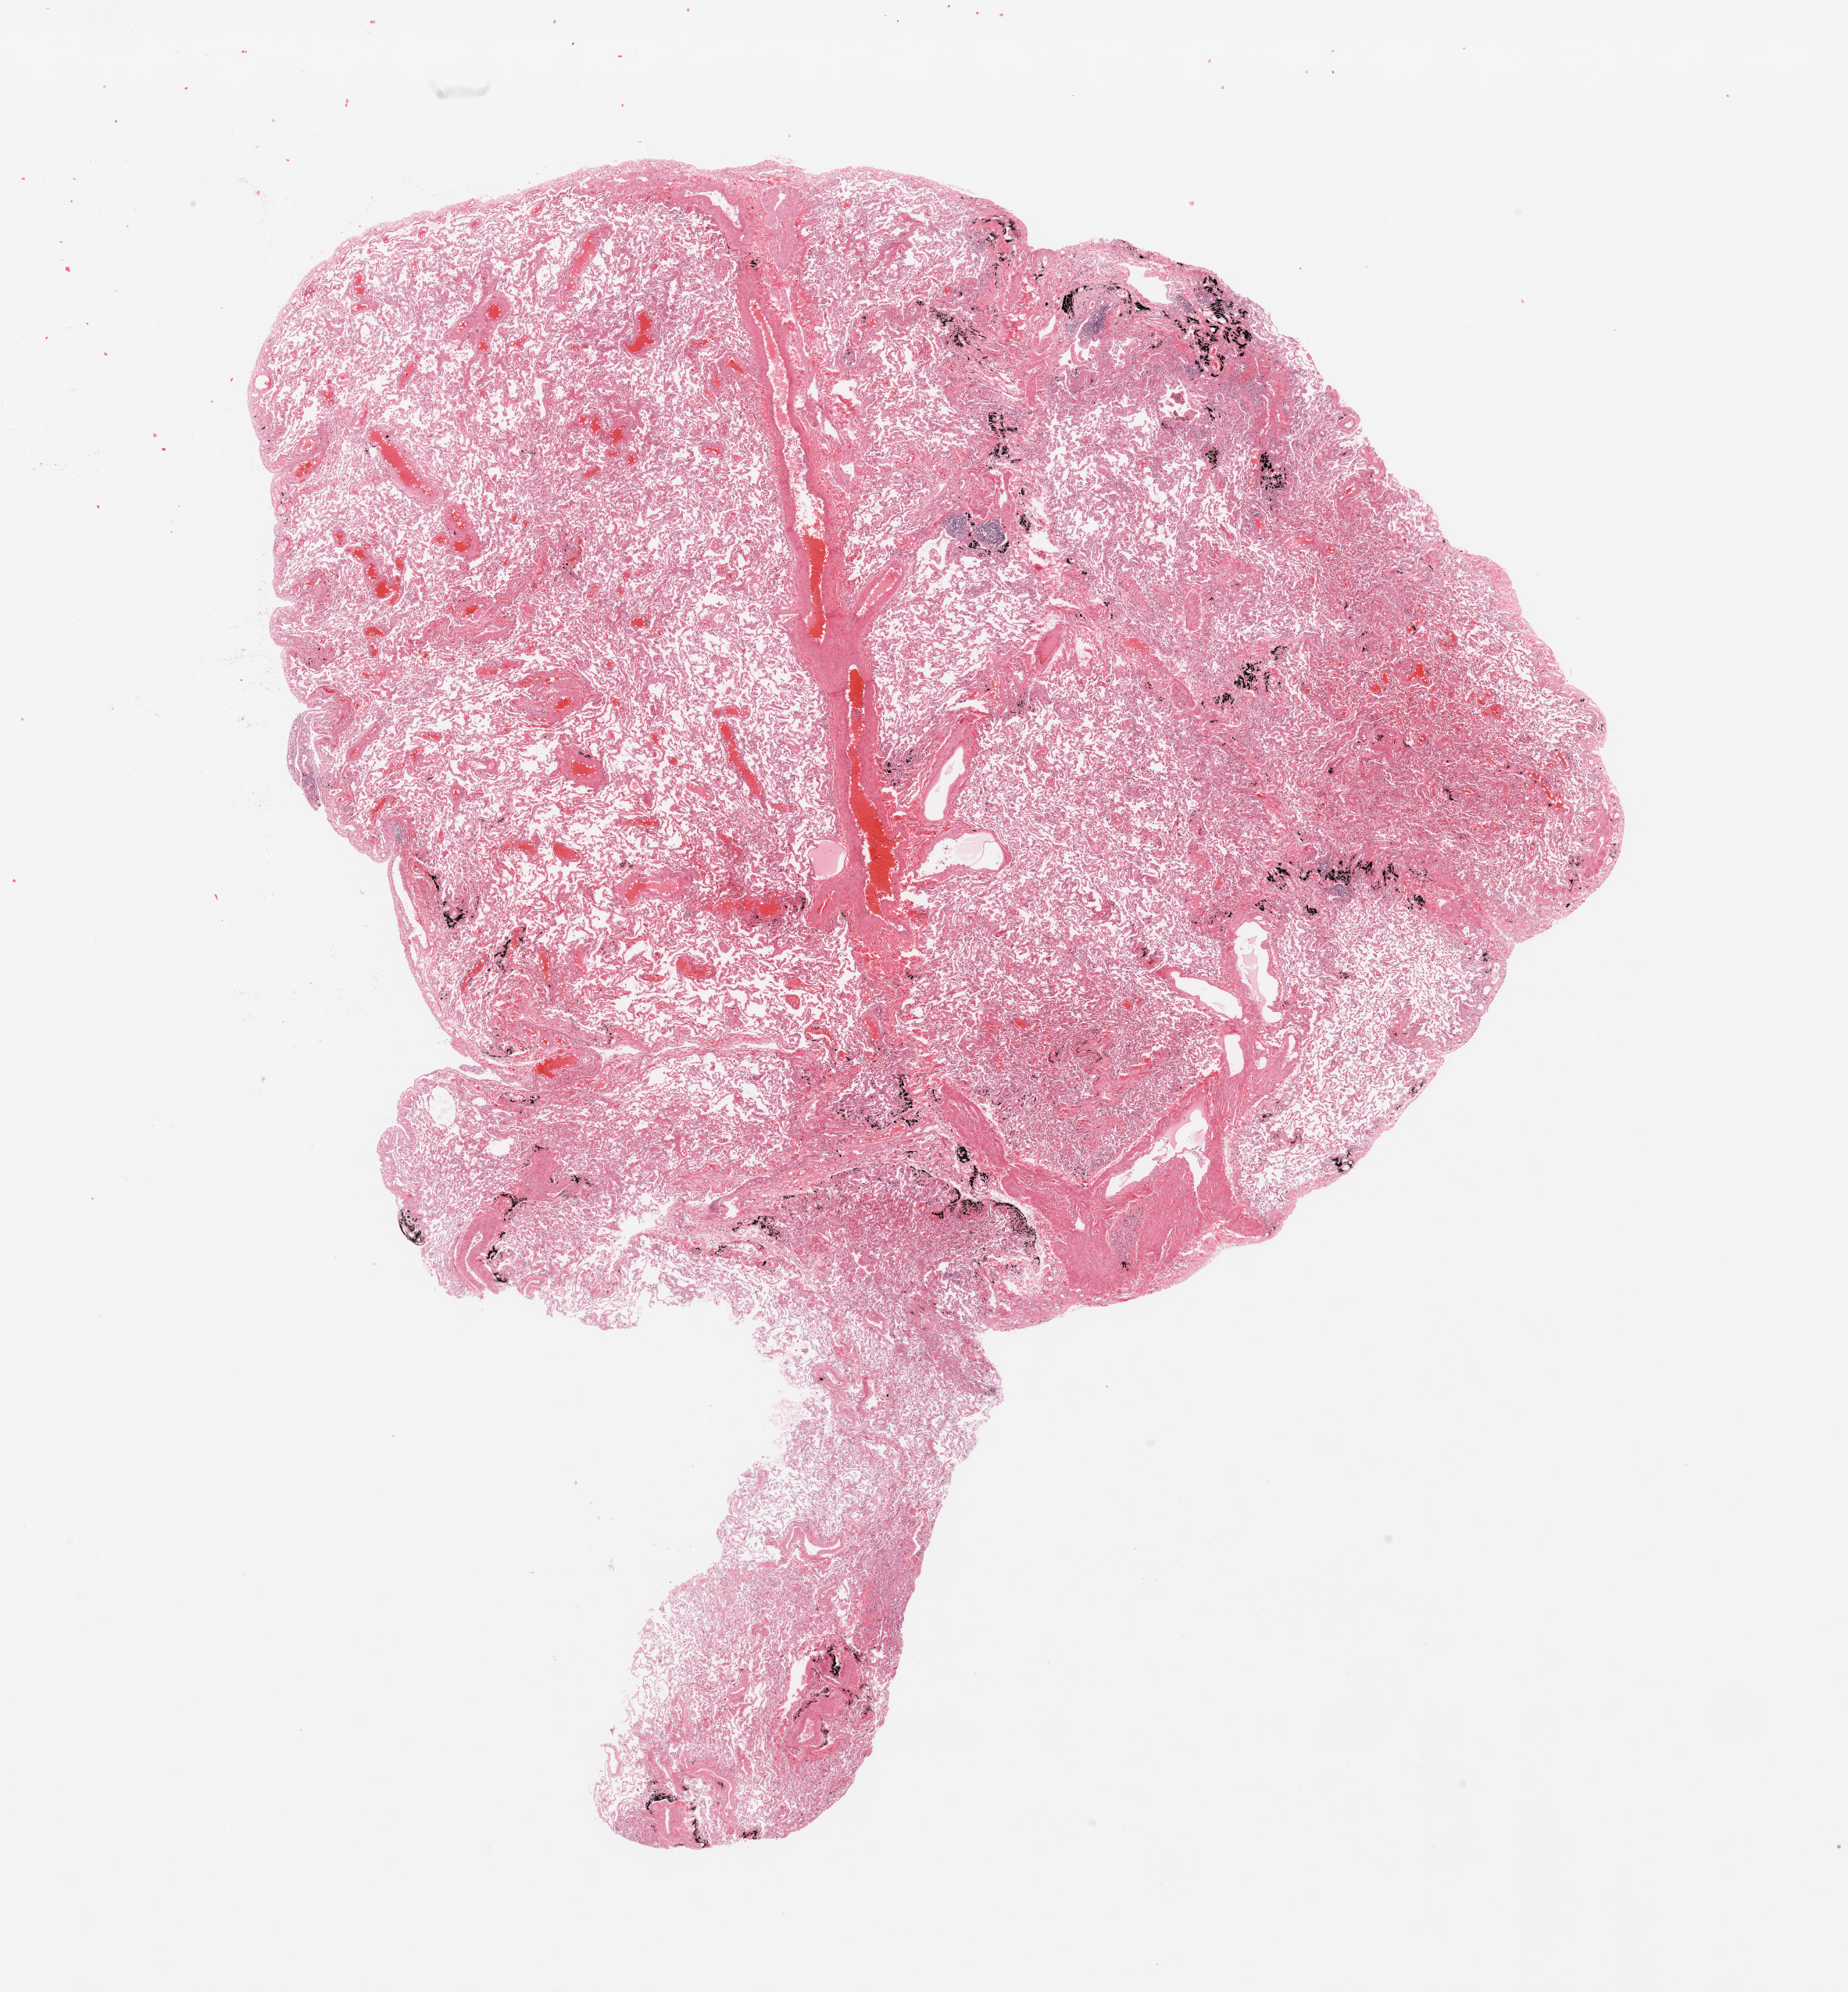
Digitized Hematoxylin and eosin (H&E) stained tissue section (whole slide), whole scanned area (about 18.7 x 20.2 mm) shown as a low-resolution overview, normal (non-tumour) tissue sample, sampled site: lung. 69-year-old male patient.
This section: normal (non-tumour) tissue from the same patient. Patient diagnosis: Adenocarcinoma, NOS.